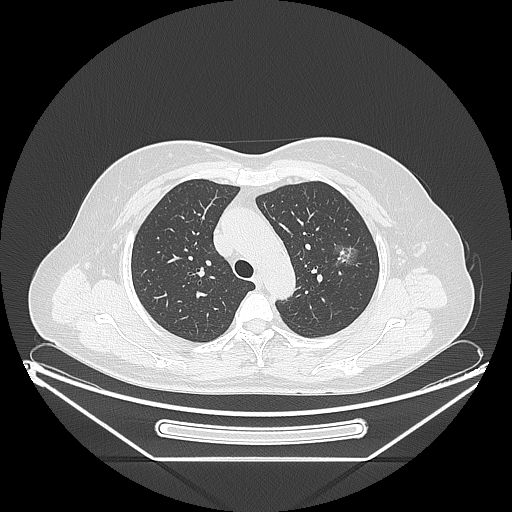
Chest CT, one axial slice; slice 159 of 226 in the series (ordered by position); reconstruction kernel LUNG; 120 kVp; lung window (W 1500 / L -600 HU); 1.25 mm slice thickness; 512 × 512 image matrix, field of view 447 × 447 mm. Female patient, age 54 years. From the clinical record (not read from this slice): clinical TNM (as recorded): T1c N0 M0; histopathological grade: G1.
Annotated regions visible in this slice (bounding box drawn by a radiologist):
- lung tumour (recorded histology: adenocarcinoma): bounding box (x1, y1, x2, y2) in pixels: (322, 237, 362, 275)